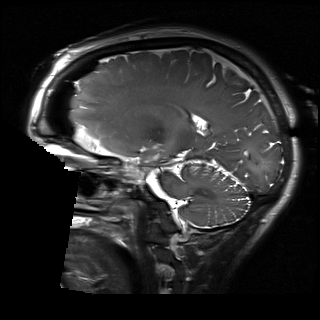
Brain MRI from a brain-tumour surgery series, one sagittal slice; 320 × 320 image matrix, field of view 230 × 230 mm. Case-level facts recorded for this patient, not image findings: histopathology: Glioblastoma; WHO grade: 2; IDH mutation: no.
Outlined on this slice (expert manual segmentation):
- residual tumour: bounding box [x1, y1, x2, y2] px = [154, 156, 156, 160]